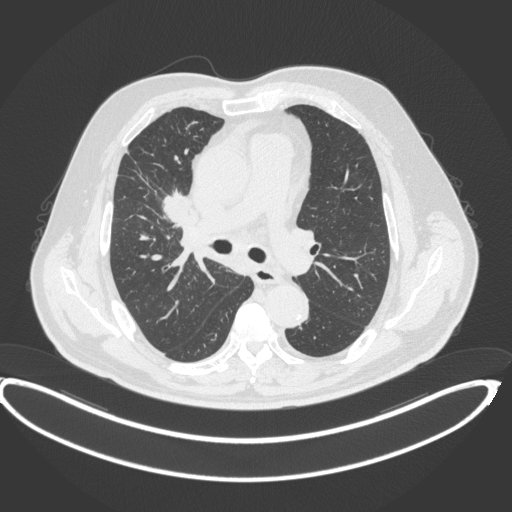
Chest CT, one axial slice. Slice 254 of 395 in the series (ordered by position). Reconstruction kernel B31f. 120 kVp. Lung window (W 1500 / L -600 HU). 1 mm slice thickness. 512 × 512 image matrix. Male patient, age 62 years. Case-level facts recorded for this patient, not image findings: clinical TNM (as recorded): T1c N3 M1c.
Outlined on this slice (rectangle marked by the reading radiologist):
- lung tumour (recorded histology: adenocarcinoma): bounding box (x1, y1, x2, y2) in pixels: (164, 188, 198, 231)